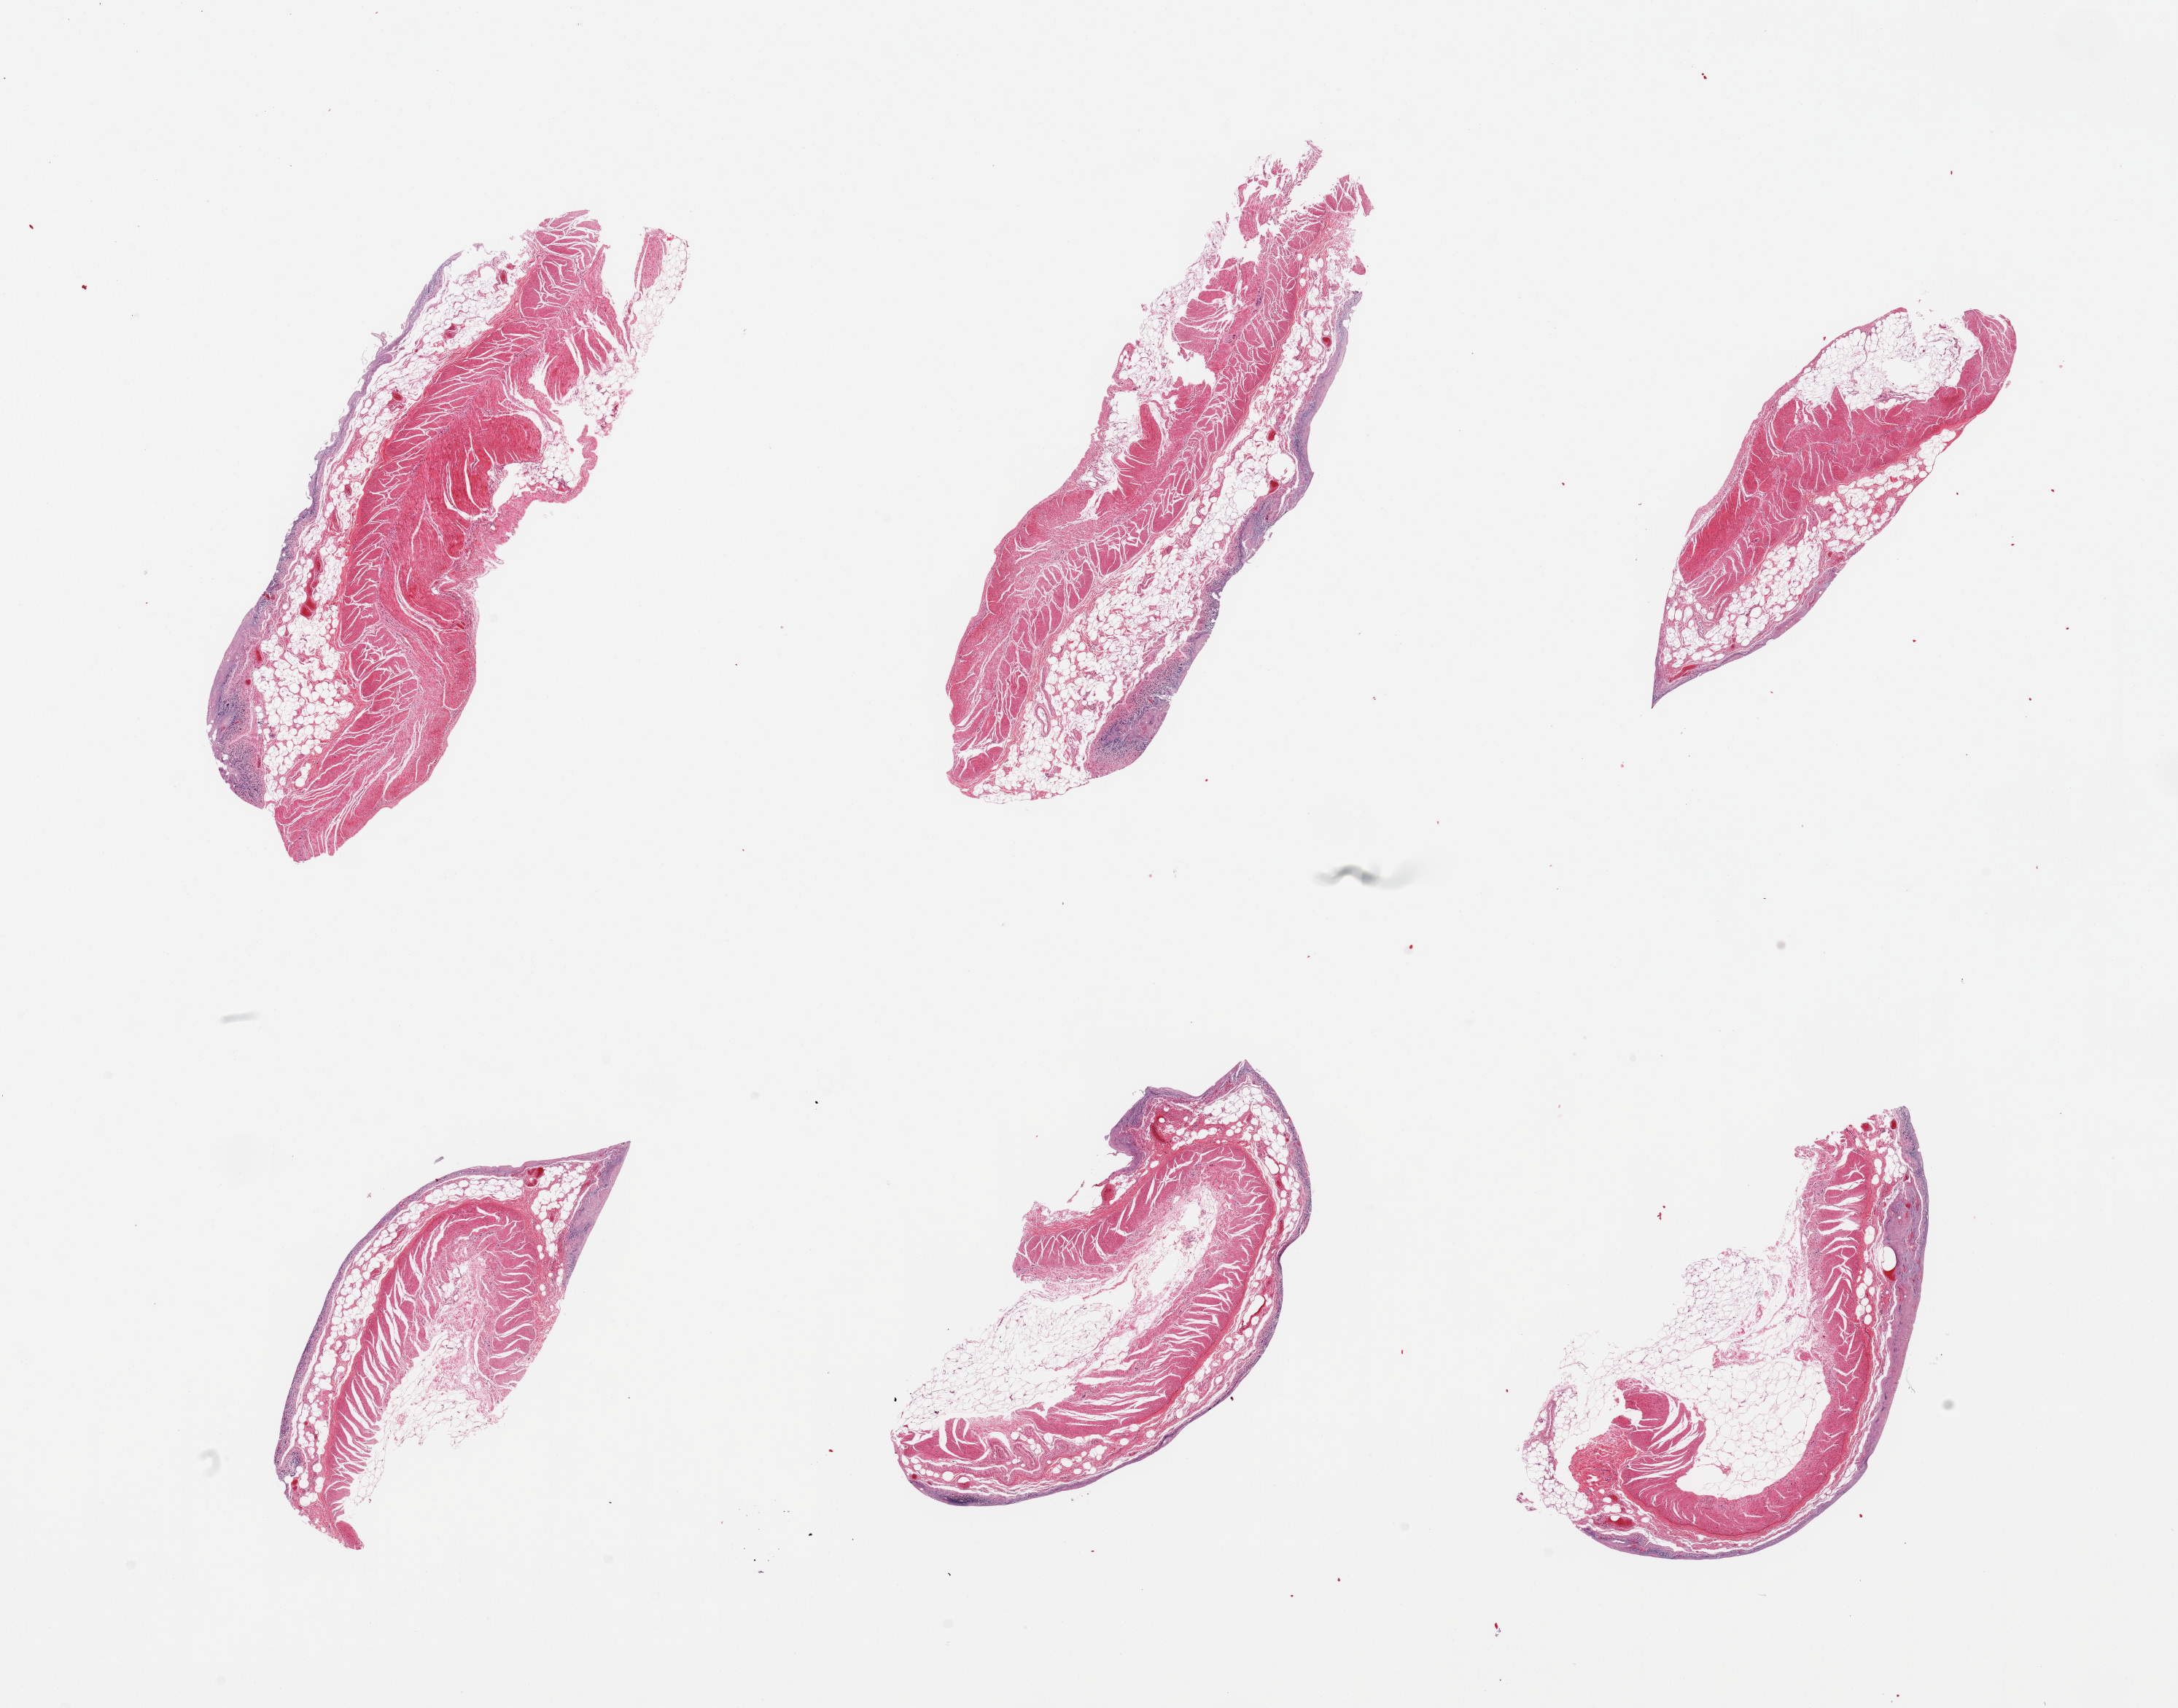
Digitized haematoxylin and eosin-stained section, whole scanned area (about 23.6 x 18.5 mm, slide scanned at 20x) shown as a low-resolution overview; PAXgene-fixed paraffin-embedded (PFPE) section; target tissue: ileum; tissue donor sample. Male donor.
Reviewer comment on this tissue sample: 6 pieces; severe autolysis of mucosa, muscularis (not target) is better preserved, lack of target lymphoid aggregates.